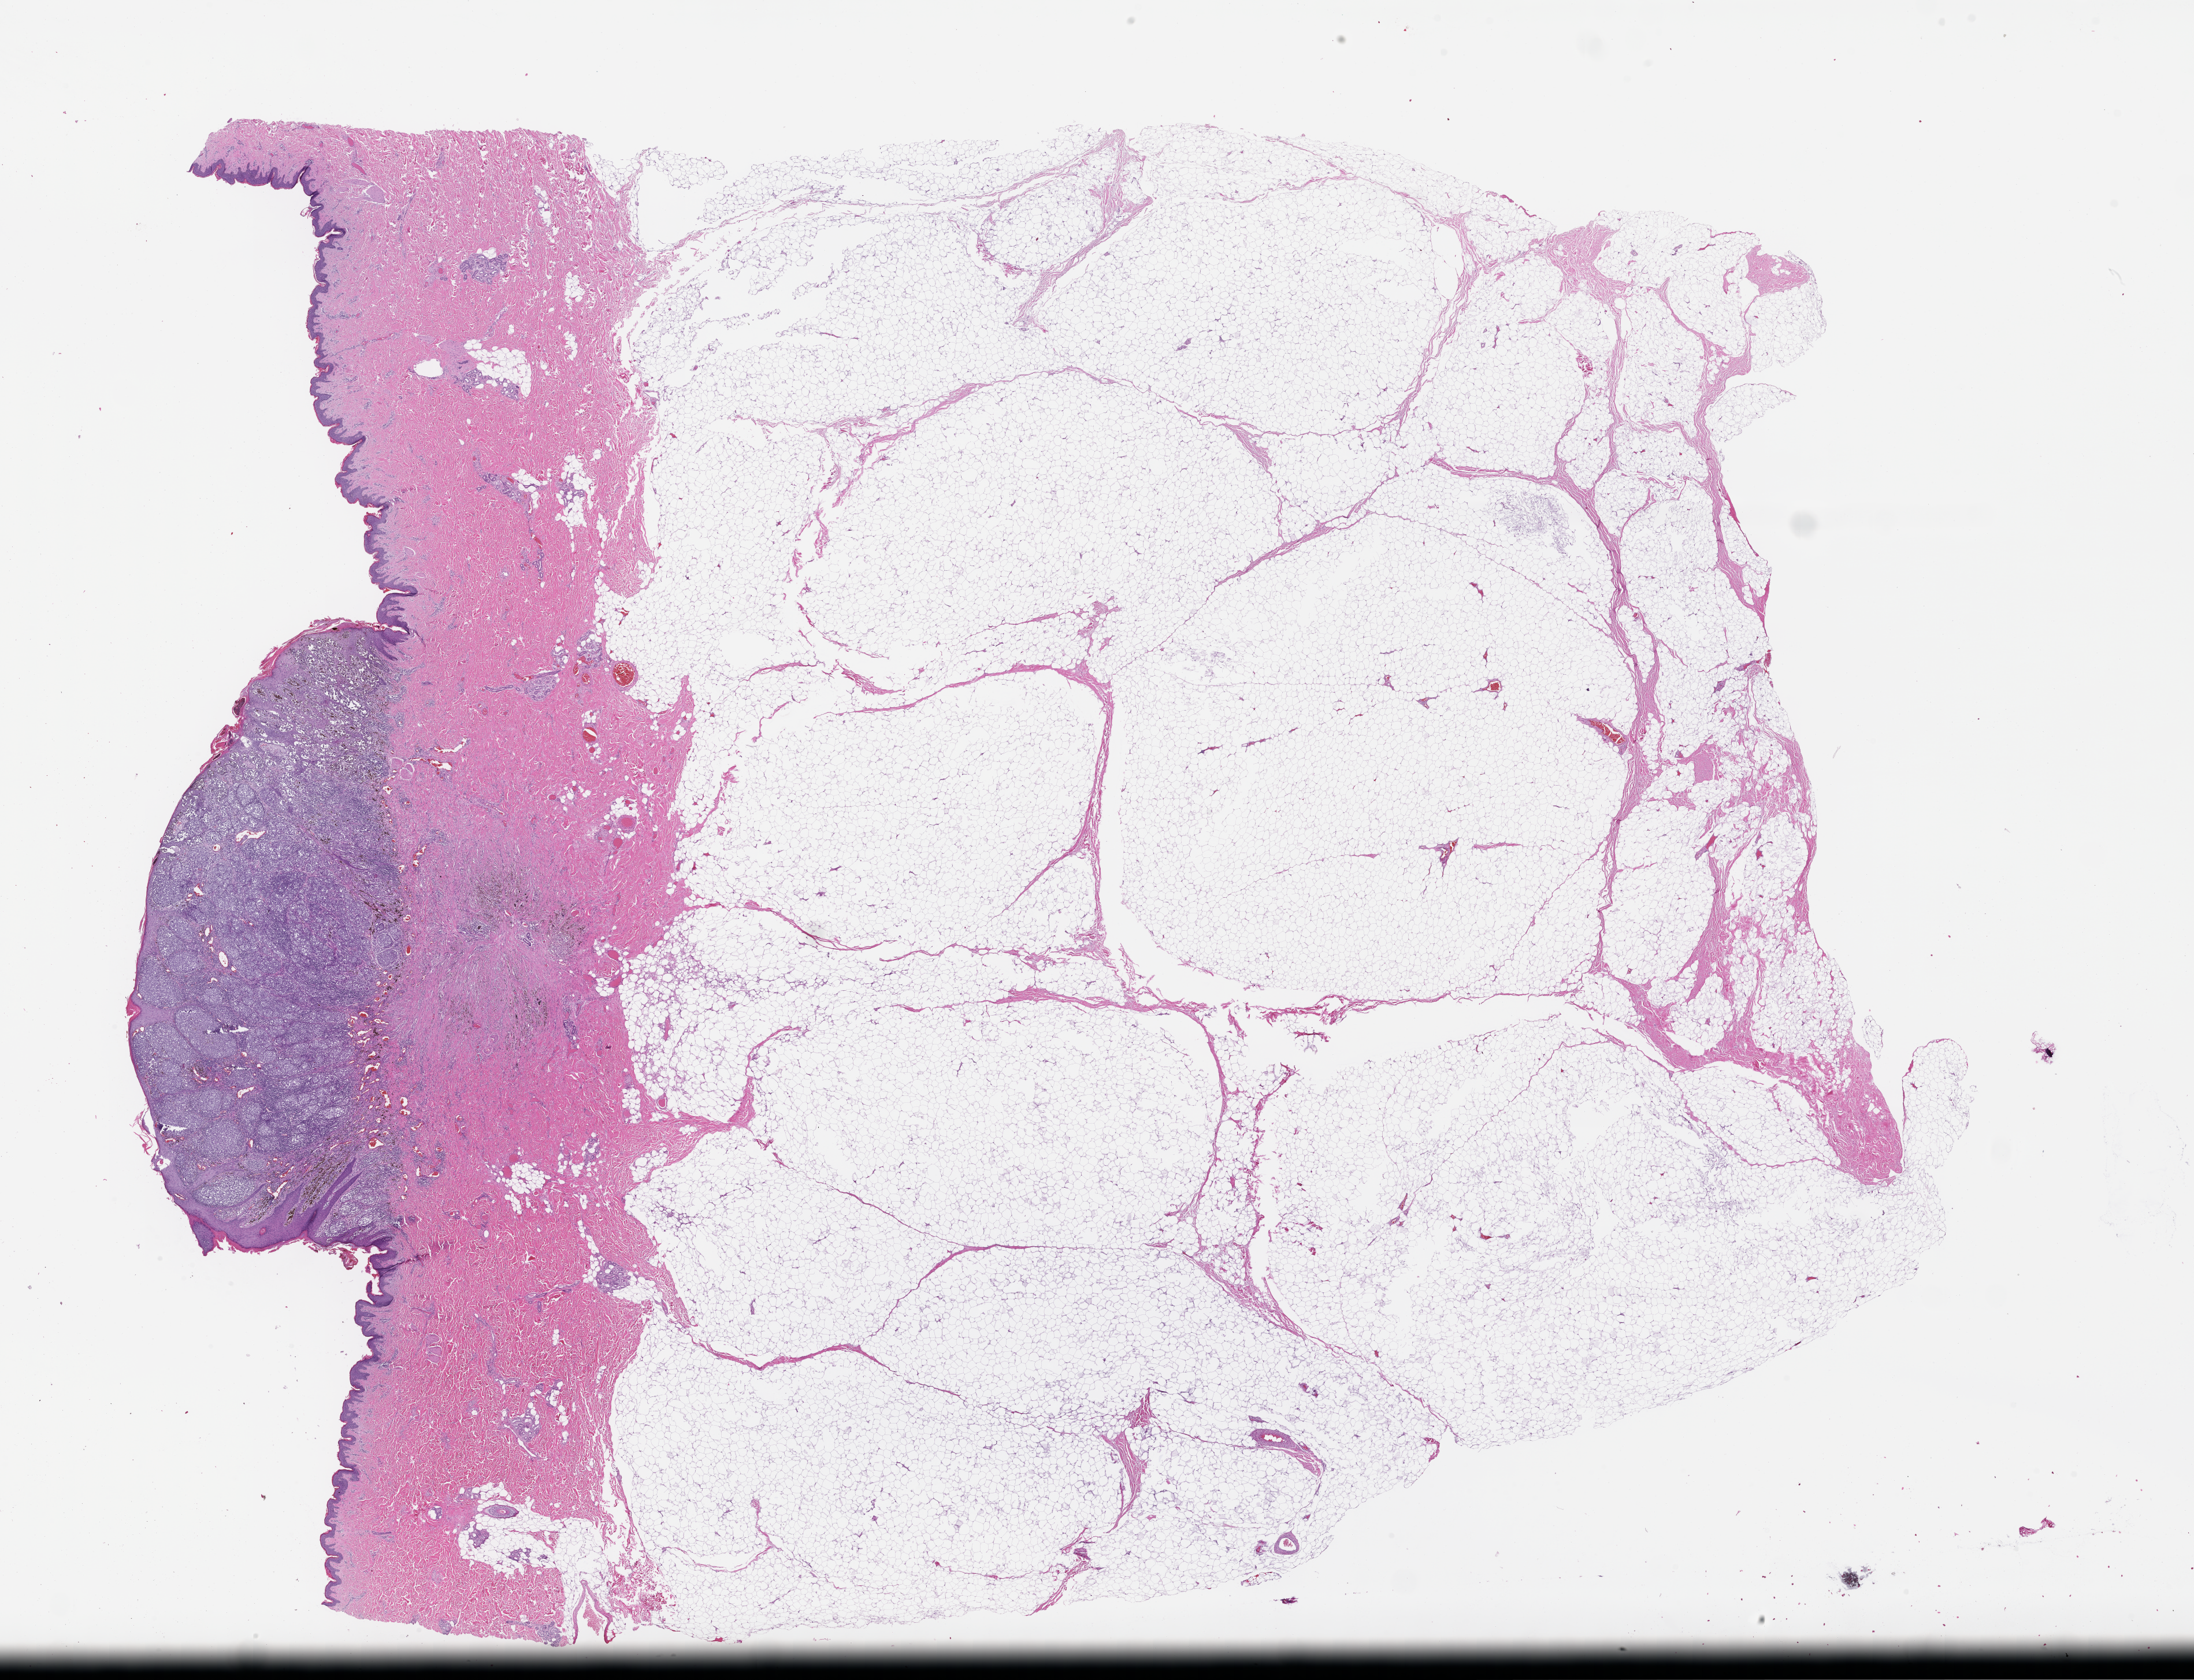
Whole-slide image, H&E stain — a low-resolution overview of the entire scanned area, about 30.7 x 23.5 mm. FFPE section. Tissue site: skin. Specimen time point: archival tissue. Patient sex: female.
This section: primary tumour tissue. Diagnosis: Melanoma.